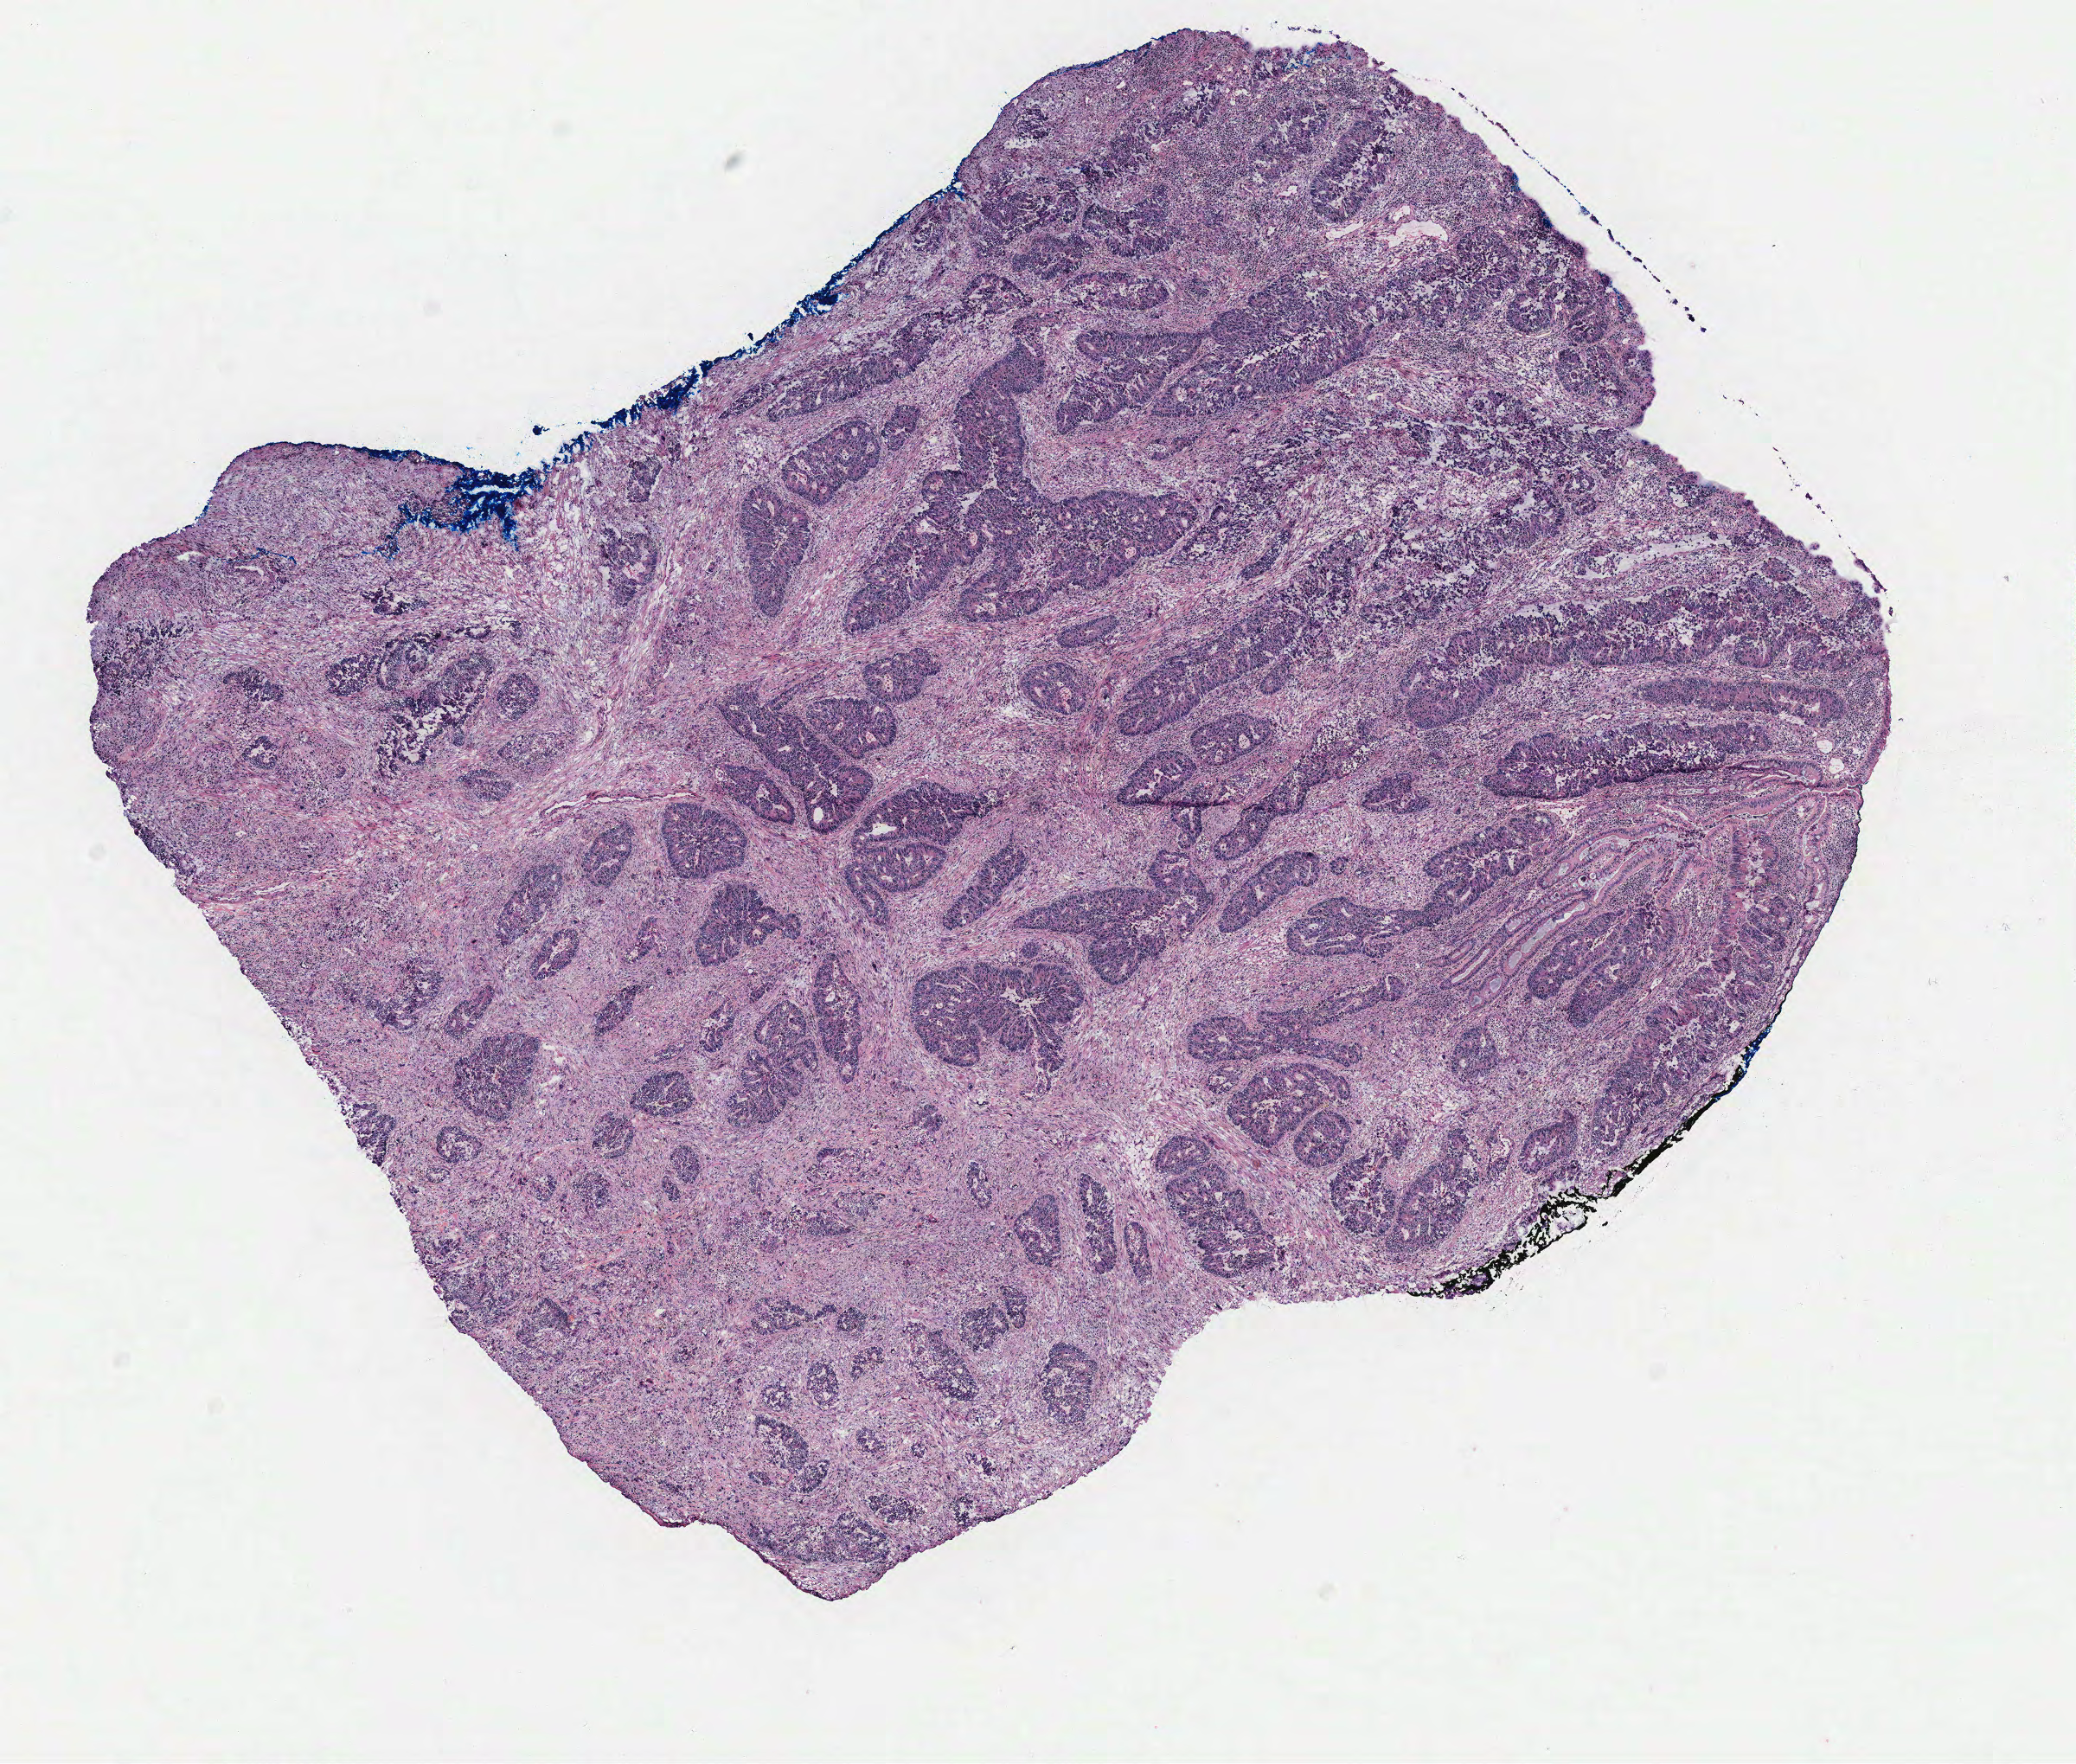
Whole-slide histology image, H&E-stained, whole scanned area (about 9.6 x 8.2 mm) shown as a low-resolution overview. Colon, tissue type not recorded. Patient sex: female.
• patient diagnosis: Adenocarcinoma, NOS (rectum, NOS)